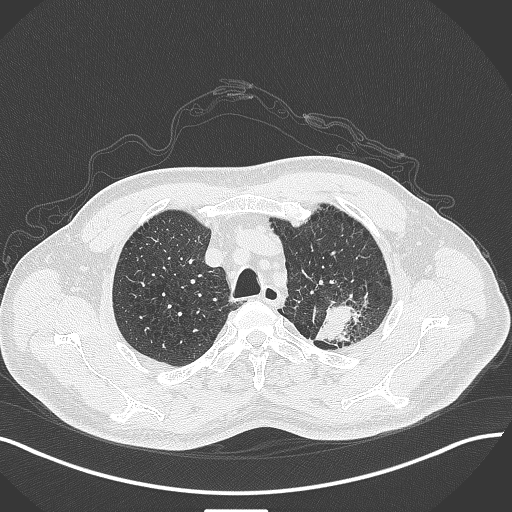
Chest CT, one axial slice; position 347 of 429 along the scan axis; reconstruction kernel B70f; lung window (W 1500 / L -600 HU); 512 × 512 image matrix, field of view 400 × 400 mm. Male patient, age 55 years. Case-level facts recorded for this patient, not image findings: clinical TNM (as recorded): T3 N0 M1c; histopathological grade: G3.
Annotated regions visible in this slice (bounding box drawn by a radiologist):
- lung tumour (recorded histology: adenocarcinoma): bounding box <313,297,372,348> (left, top, right, bottom; pixels)